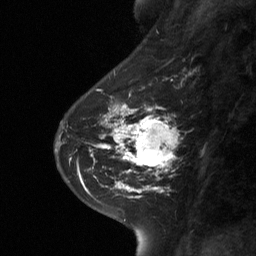
Breast MRI (dynamic contrast-enhanced), one sagittal slice. Slice 24 of 64 in the series (ordered by position). Dynamic contrast-enhanced study with each time point stored as its own series, time point 2 of 3 at this slice position (early post-contrast, ordered by acquisition time). 1.5 T. TE 4.8 ms, TR 27 ms. 2 mm slice thickness. 256 × 256 image matrix, field of view 180 × 180 mm. Female patient, age 42 years. Case-level facts recorded for this patient, not image findings: setting: breast cancer imaged before/during neoadjuvant chemotherapy; receptor status: triple-negative.
Structures marked on this image (semi-automatic segmentation, software-assisted and operator-edited):
- analysis volume of interest (the breast-tissue region the enhancement analysis was run in; not a lesion): box from (x=111, y=104) to (x=178, y=178) px
- tumour enhancement mask (voxels above the 90 % enhancement threshold inside the analysis volume of interest): (x=111, y=104)–(x=176, y=175)